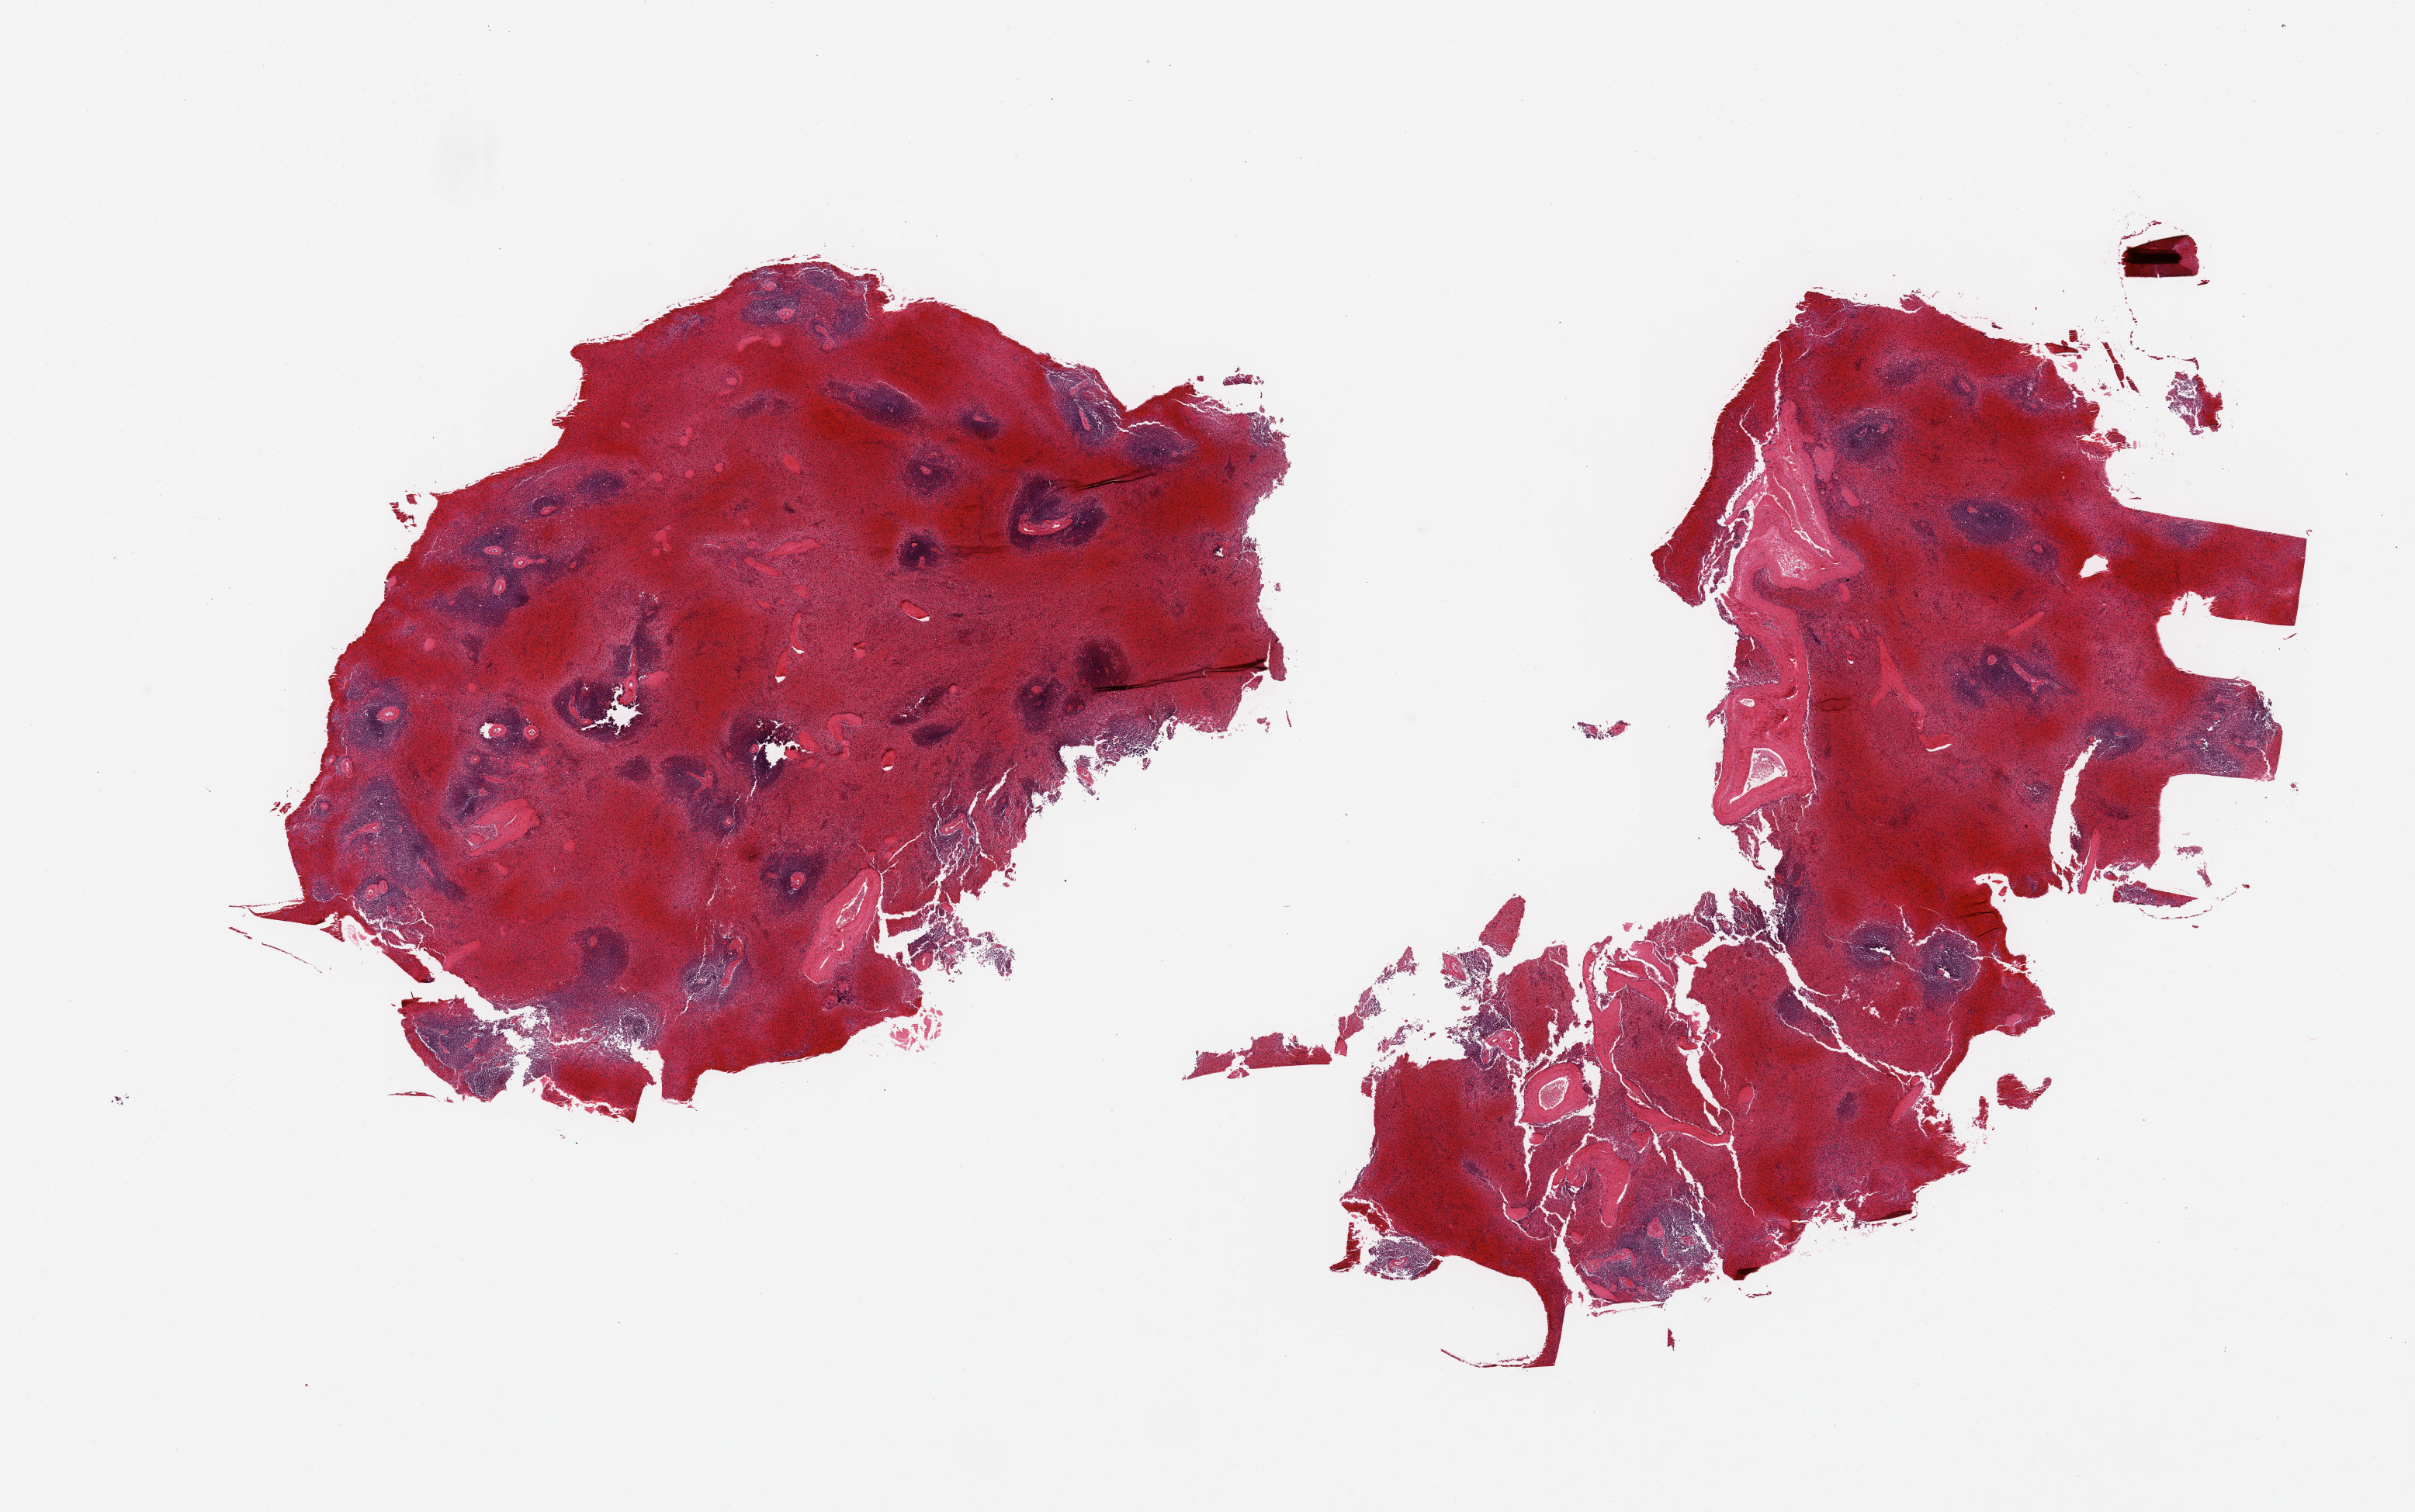
Digitized haematoxylin and eosin-stained section — a low-resolution overview of the entire scanned area, about 24.6 x 15.4 mm (slide scanned at 20x); PAXgene-fixed, paraffin-embedded tissue; target tissue: spleen; tissue donor sample. Male donor.
- reviewer comment on this tissue sample: 2 pieces; severe vascular congestion; 1 piece fragmented